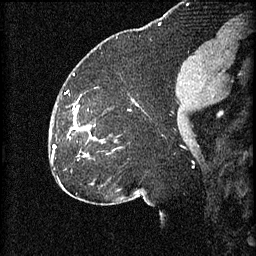
Breast MRI (dynamic contrast-enhanced), one sagittal slice. Position 32 of 60 along the scan axis. 3 images stored at this slice position (order not interpretable as contrast timing). 1.5 T. TE 4.2 ms, TR 8.2 ms. 2 mm slice thickness. 256 × 256 image matrix. Patient: female, 32 years.
Structures marked on this image (semi-automatic segmentation, software-assisted and operator-edited):
- analysis volume of interest (the breast-tissue region the enhancement analysis was run in; not a lesion): bounding box <68,108,105,157> (left, top, right, bottom; pixels)
- tumour enhancement mask (voxels above the 70 % enhancement threshold inside the analysis volume of interest): <74,108,90,135>